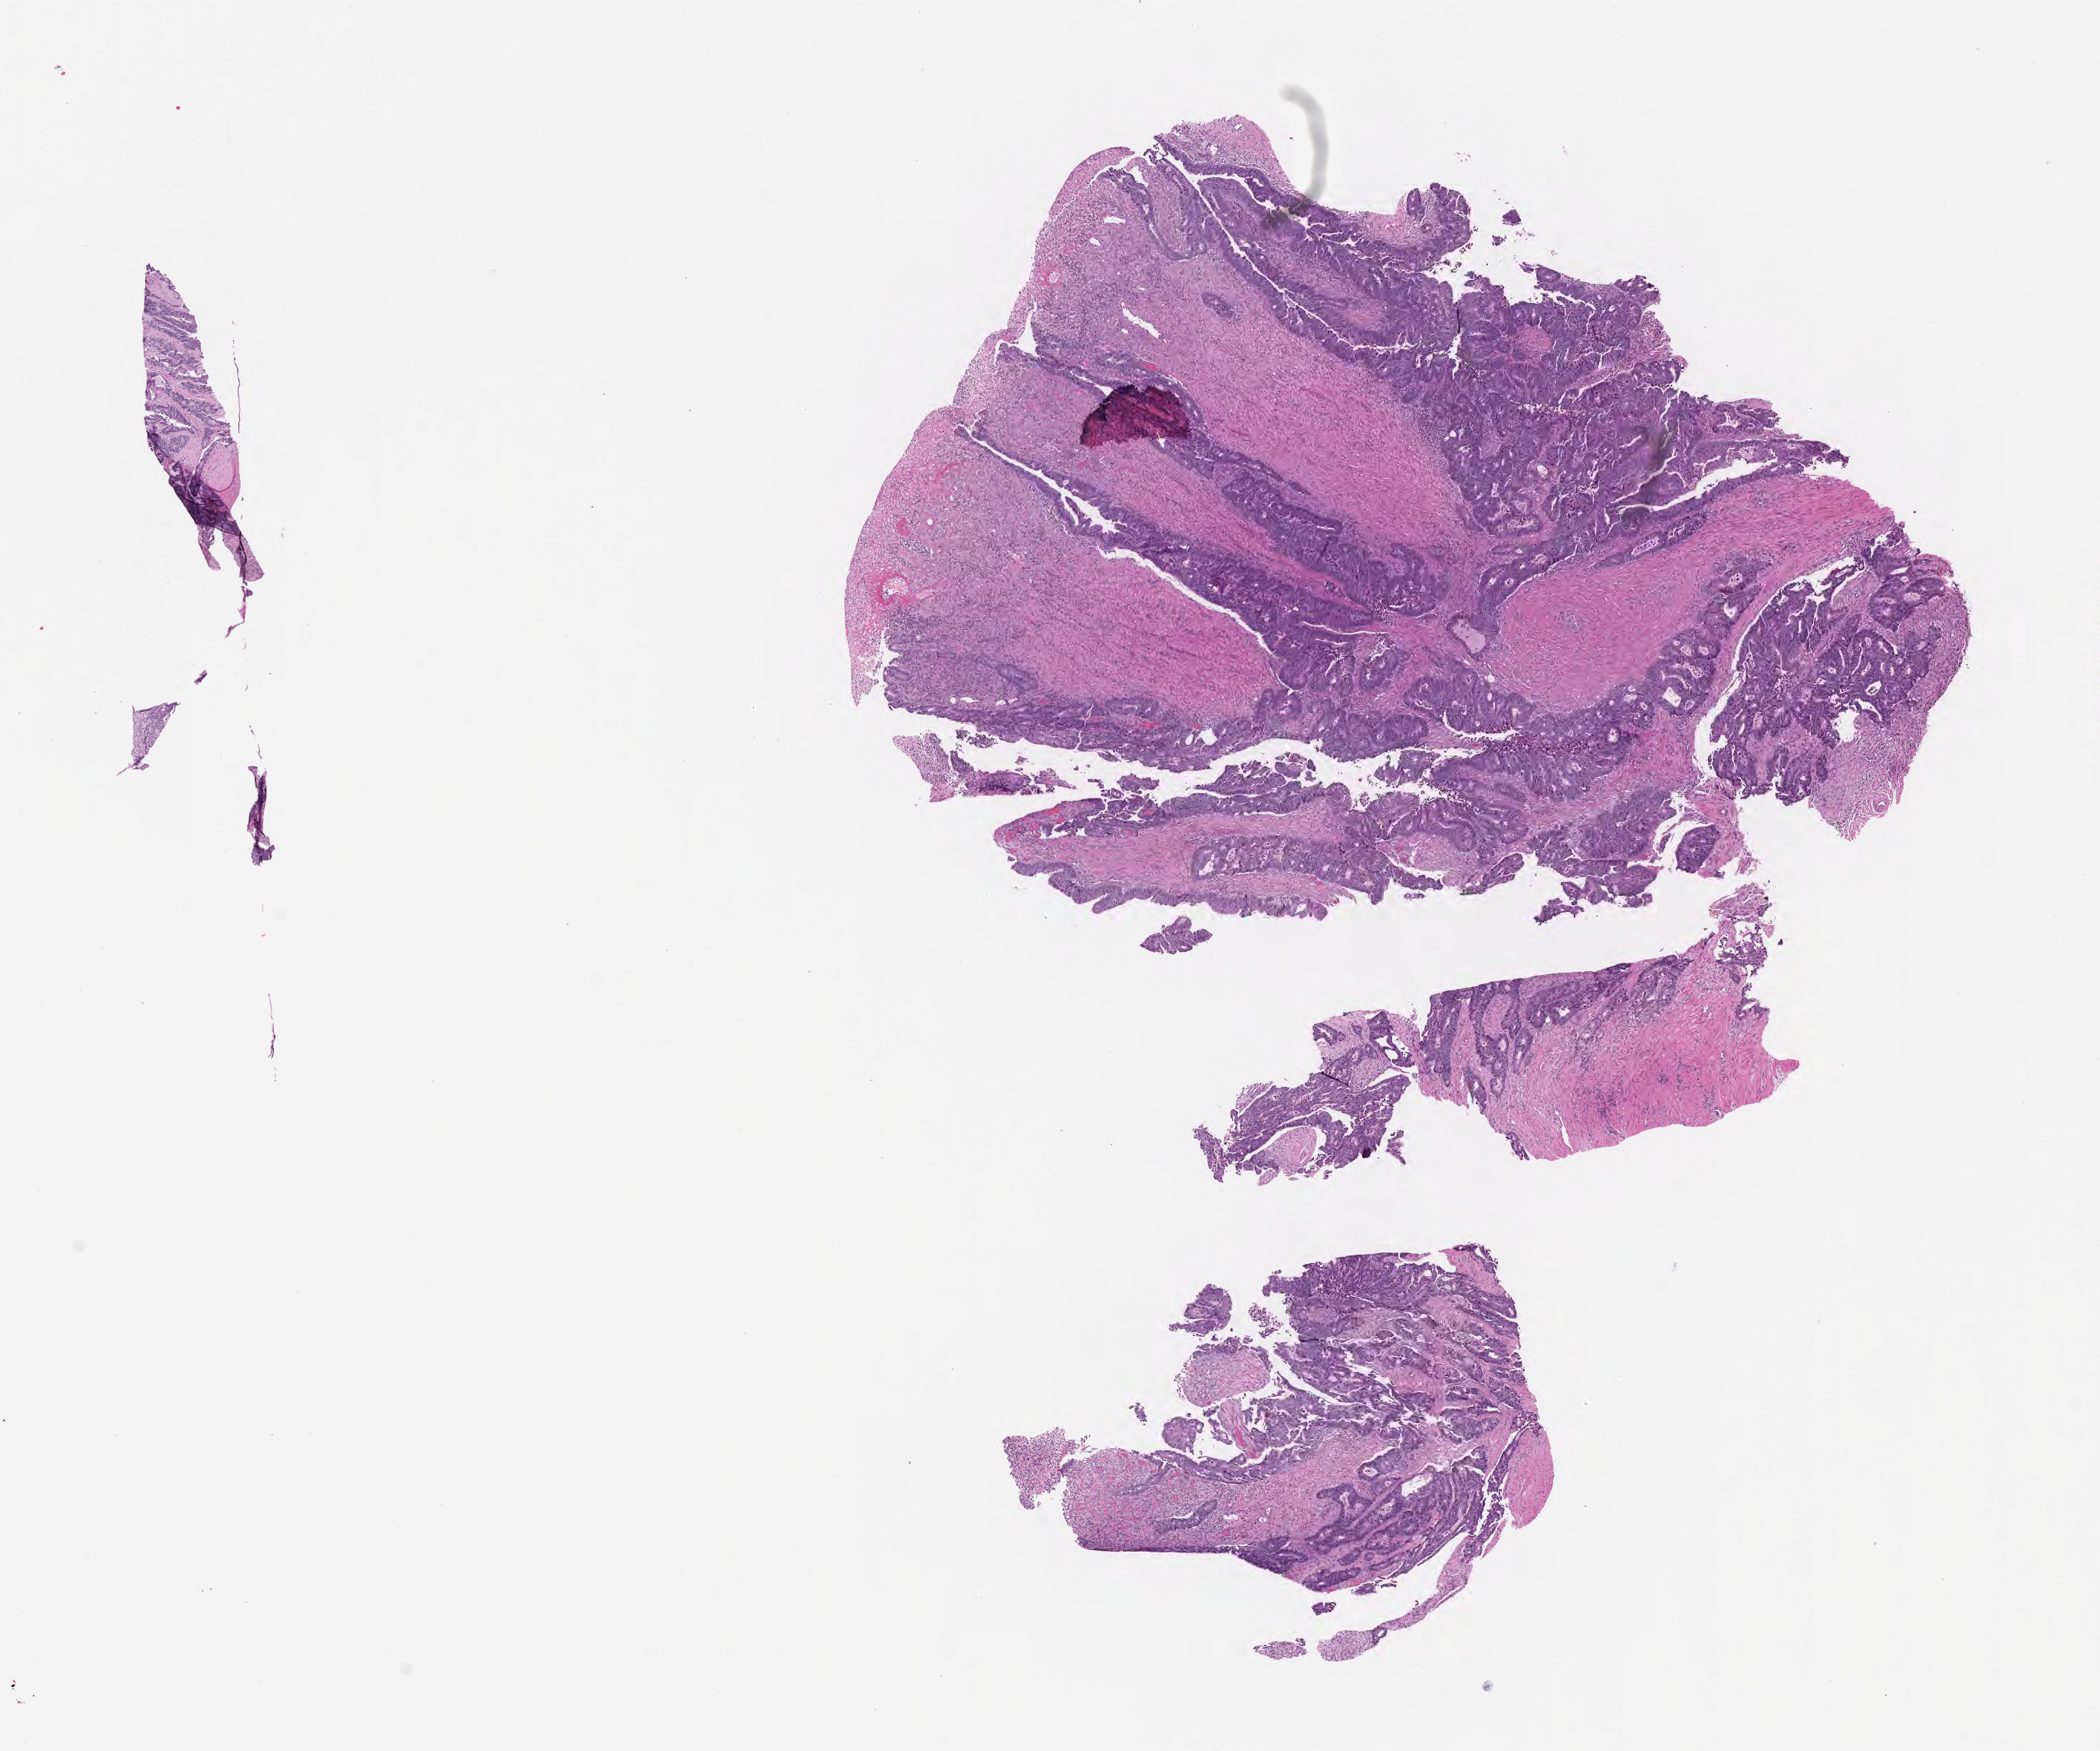
Whole-slide image, haematoxylin and eosin stain, shown as a low-resolution overview of the whole scanned area (about 11.1 x 9.2 mm). Formalin-fixed paraffin-embedded section. Primary tumor. Site: rectosigmoid junction. Female, age 69 years at initial diagnosis. Slide review estimates, as recorded: tumor cells 100%, tumor nuclei 78%.
Diagnosis: Adenocarcinoma, NOS.